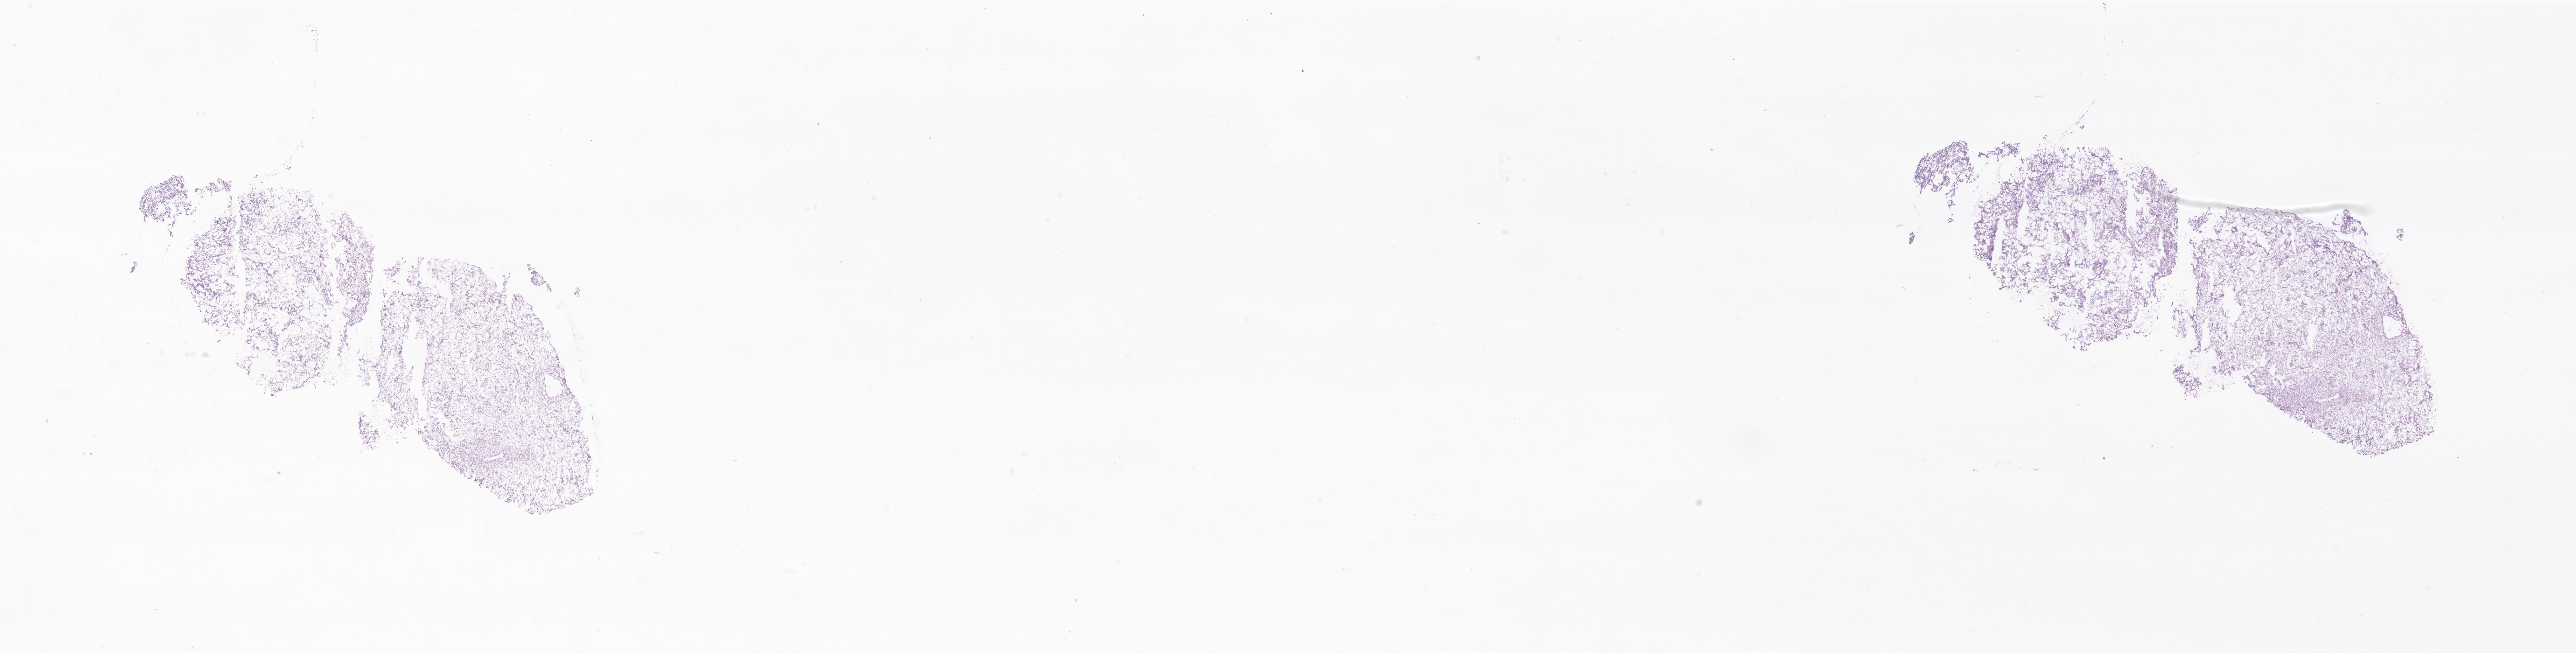
H&E whole-slide image of tumor tissue from the lung, low-resolution overview of the scanned area, about 34.1 x 8.7 mm; frozen section (OCT-embedded). Patient female; age 131 months (10 years 11 months).
Diagnosis (ICD-O-3 morphology term): Malignant tumor, spindle cell type.